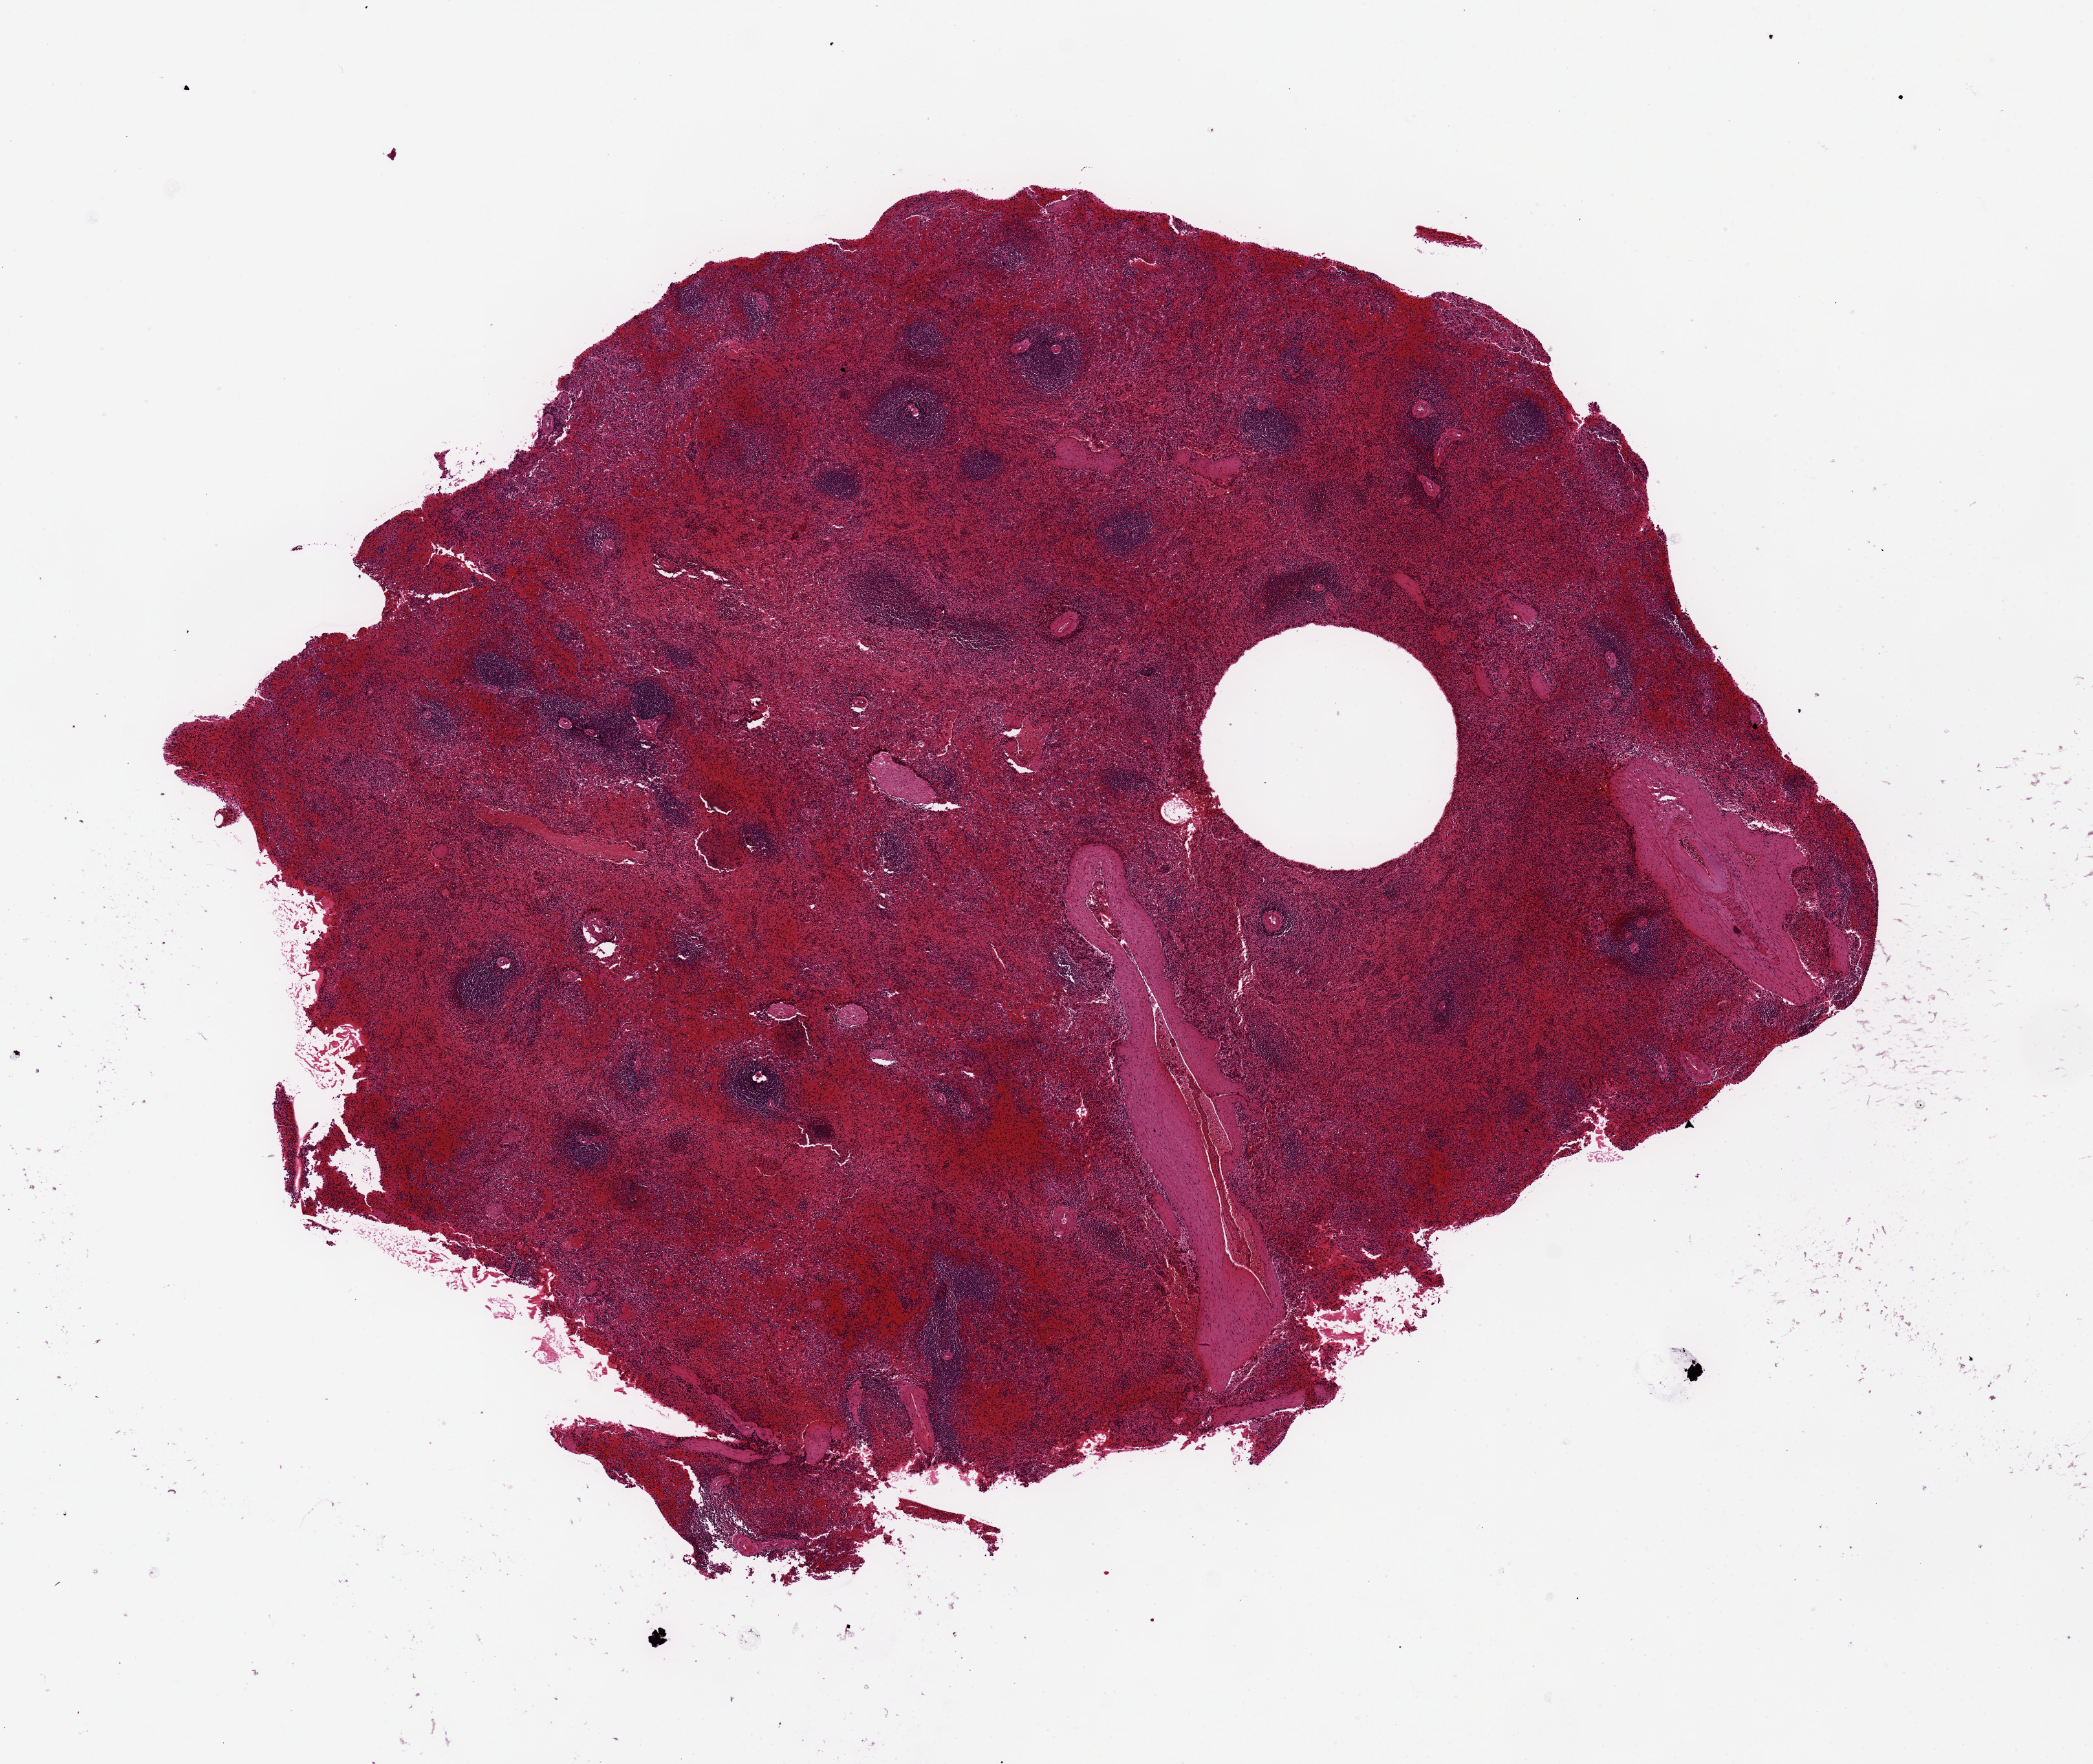
H&E whole-slide image, brightfield, shown as a low-resolution overview of the whole scanned area (about 12.8 x 10.8 mm). PAXgene-fixed, paraffin-embedded tissue. Section of spleen (target tissue). Donor tissue sample. Female donor.
Reviewer comment on this tissue sample: moderate congestion.